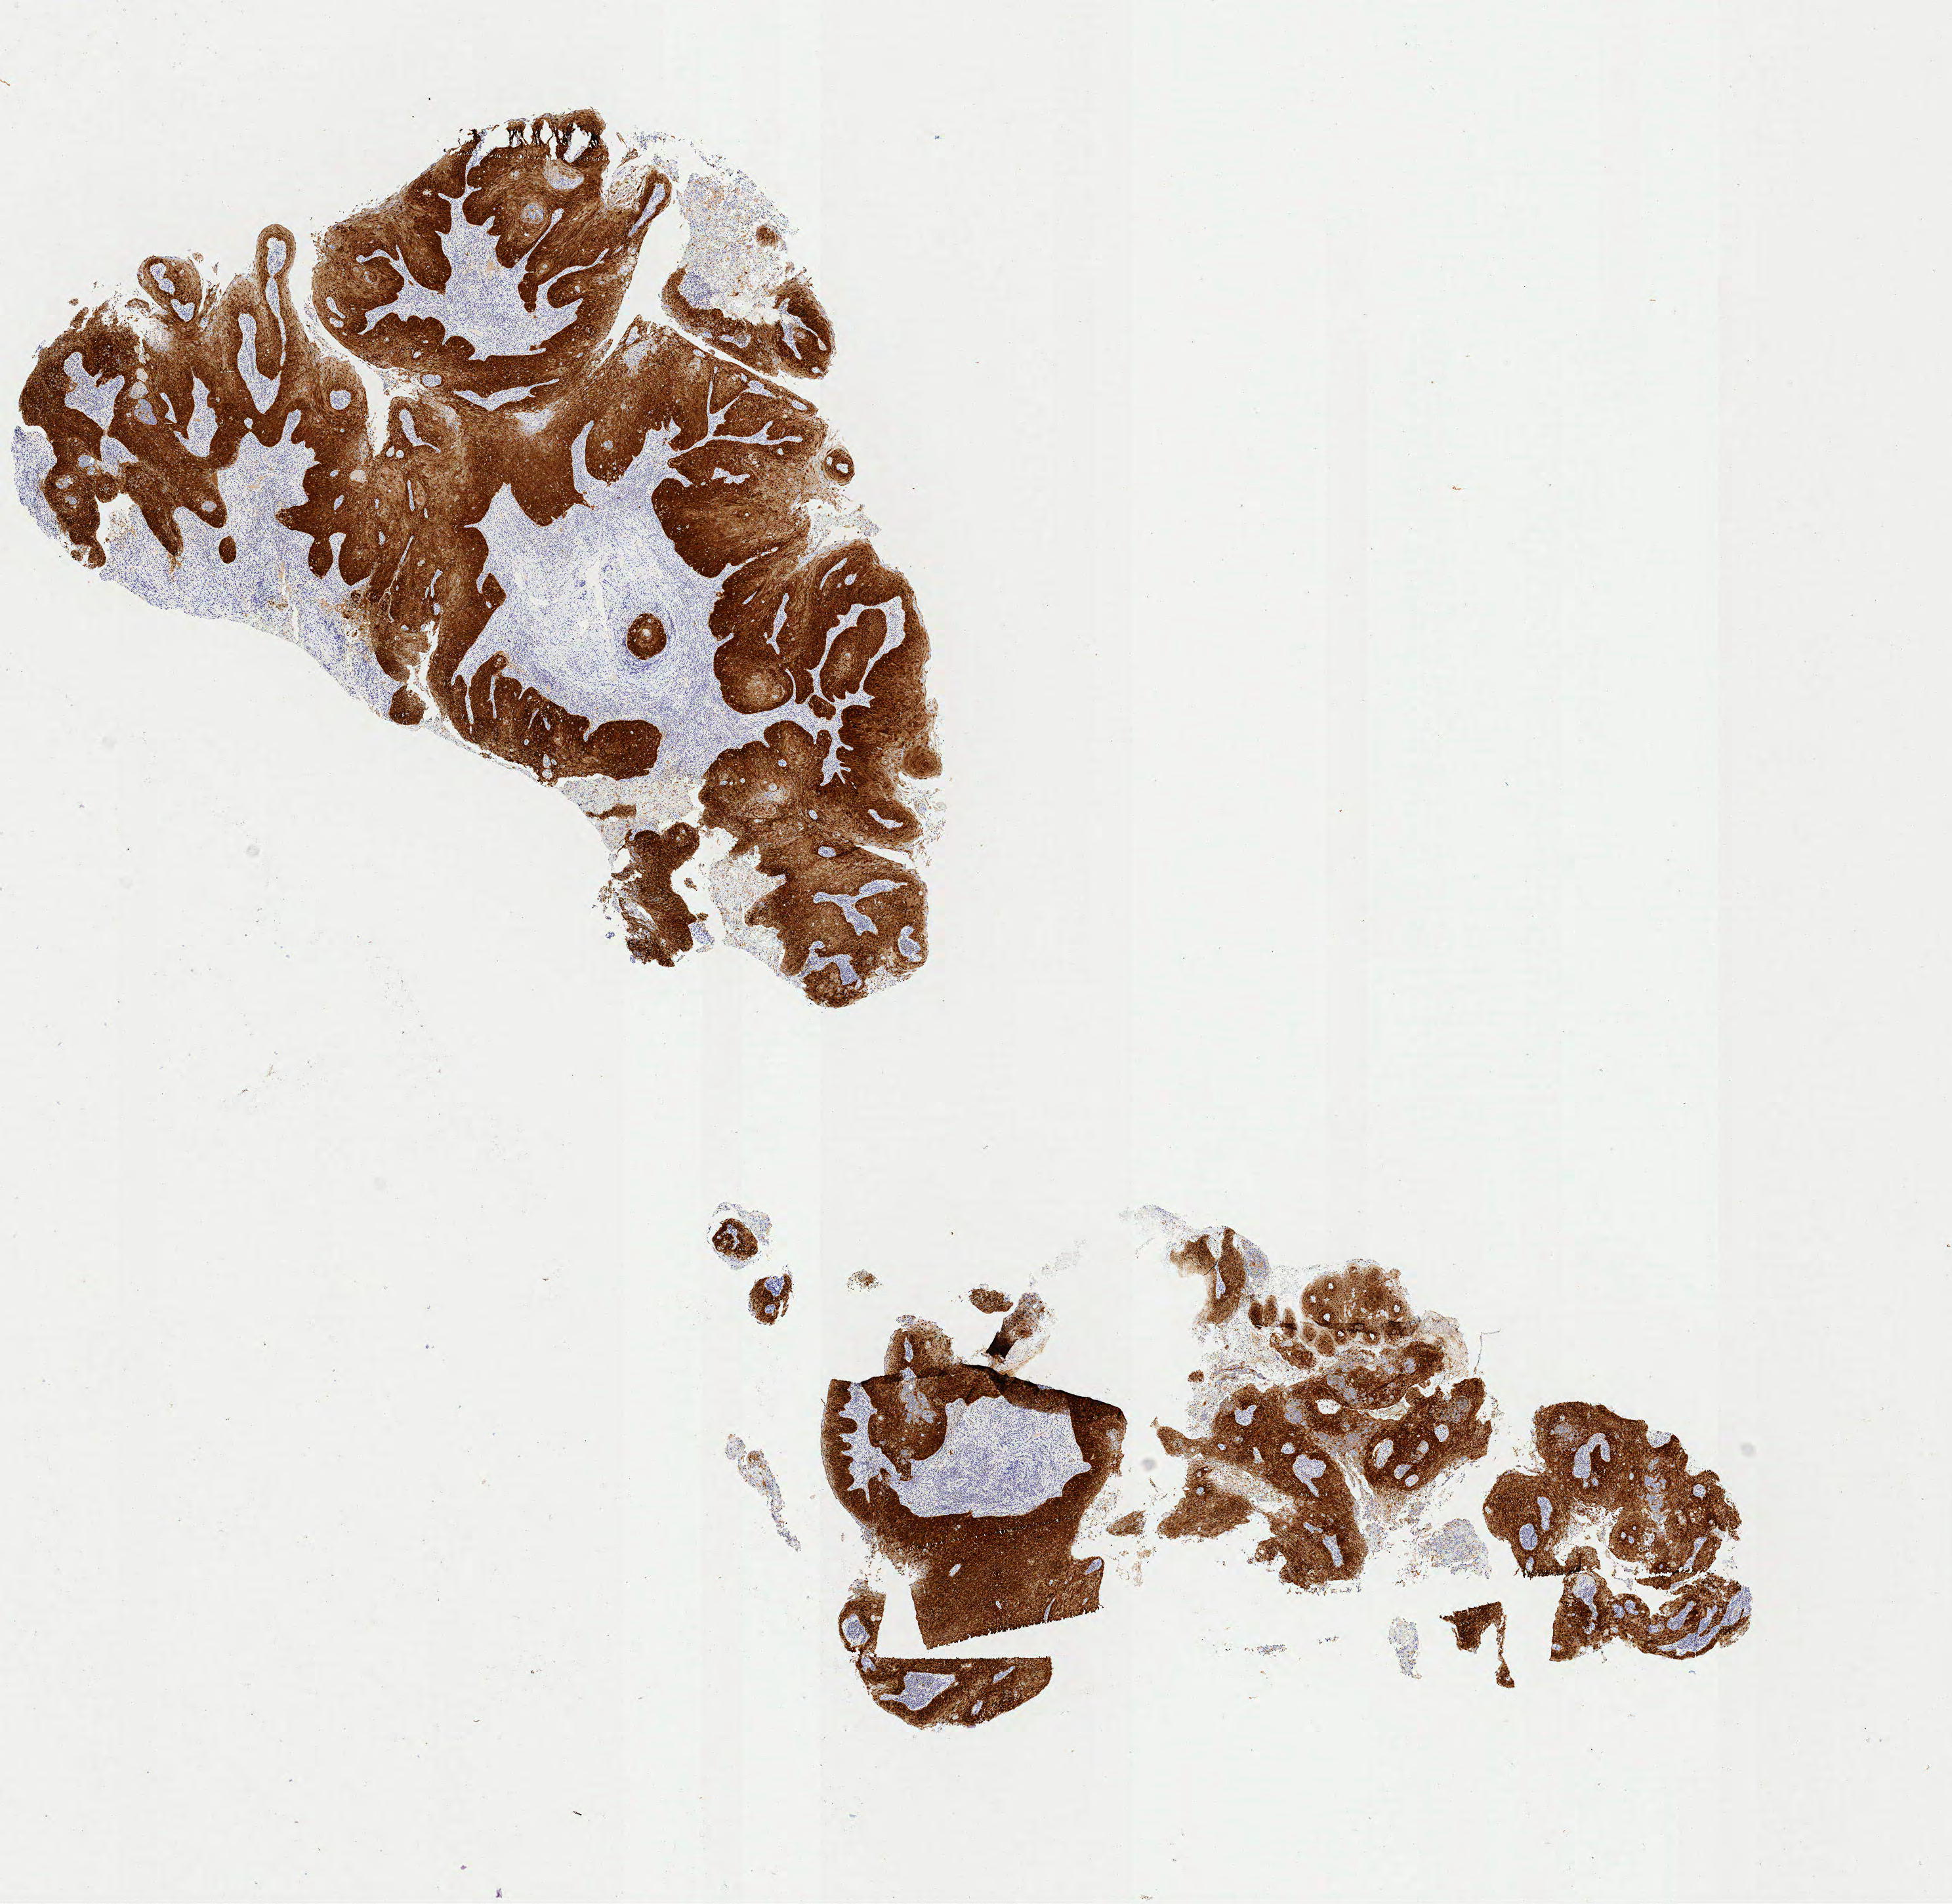
IHC for p16 (p16INK4a), whole-slide image — shown as a low-resolution overview of the whole scanned area (about 11.7 x 11.5 mm). Specimen: tumor tissue. Anatomic site: cervix. Female patient, age 29 years.
Histologic diagnosis: Squamous cell carcinoma, keratinizing, NOS.